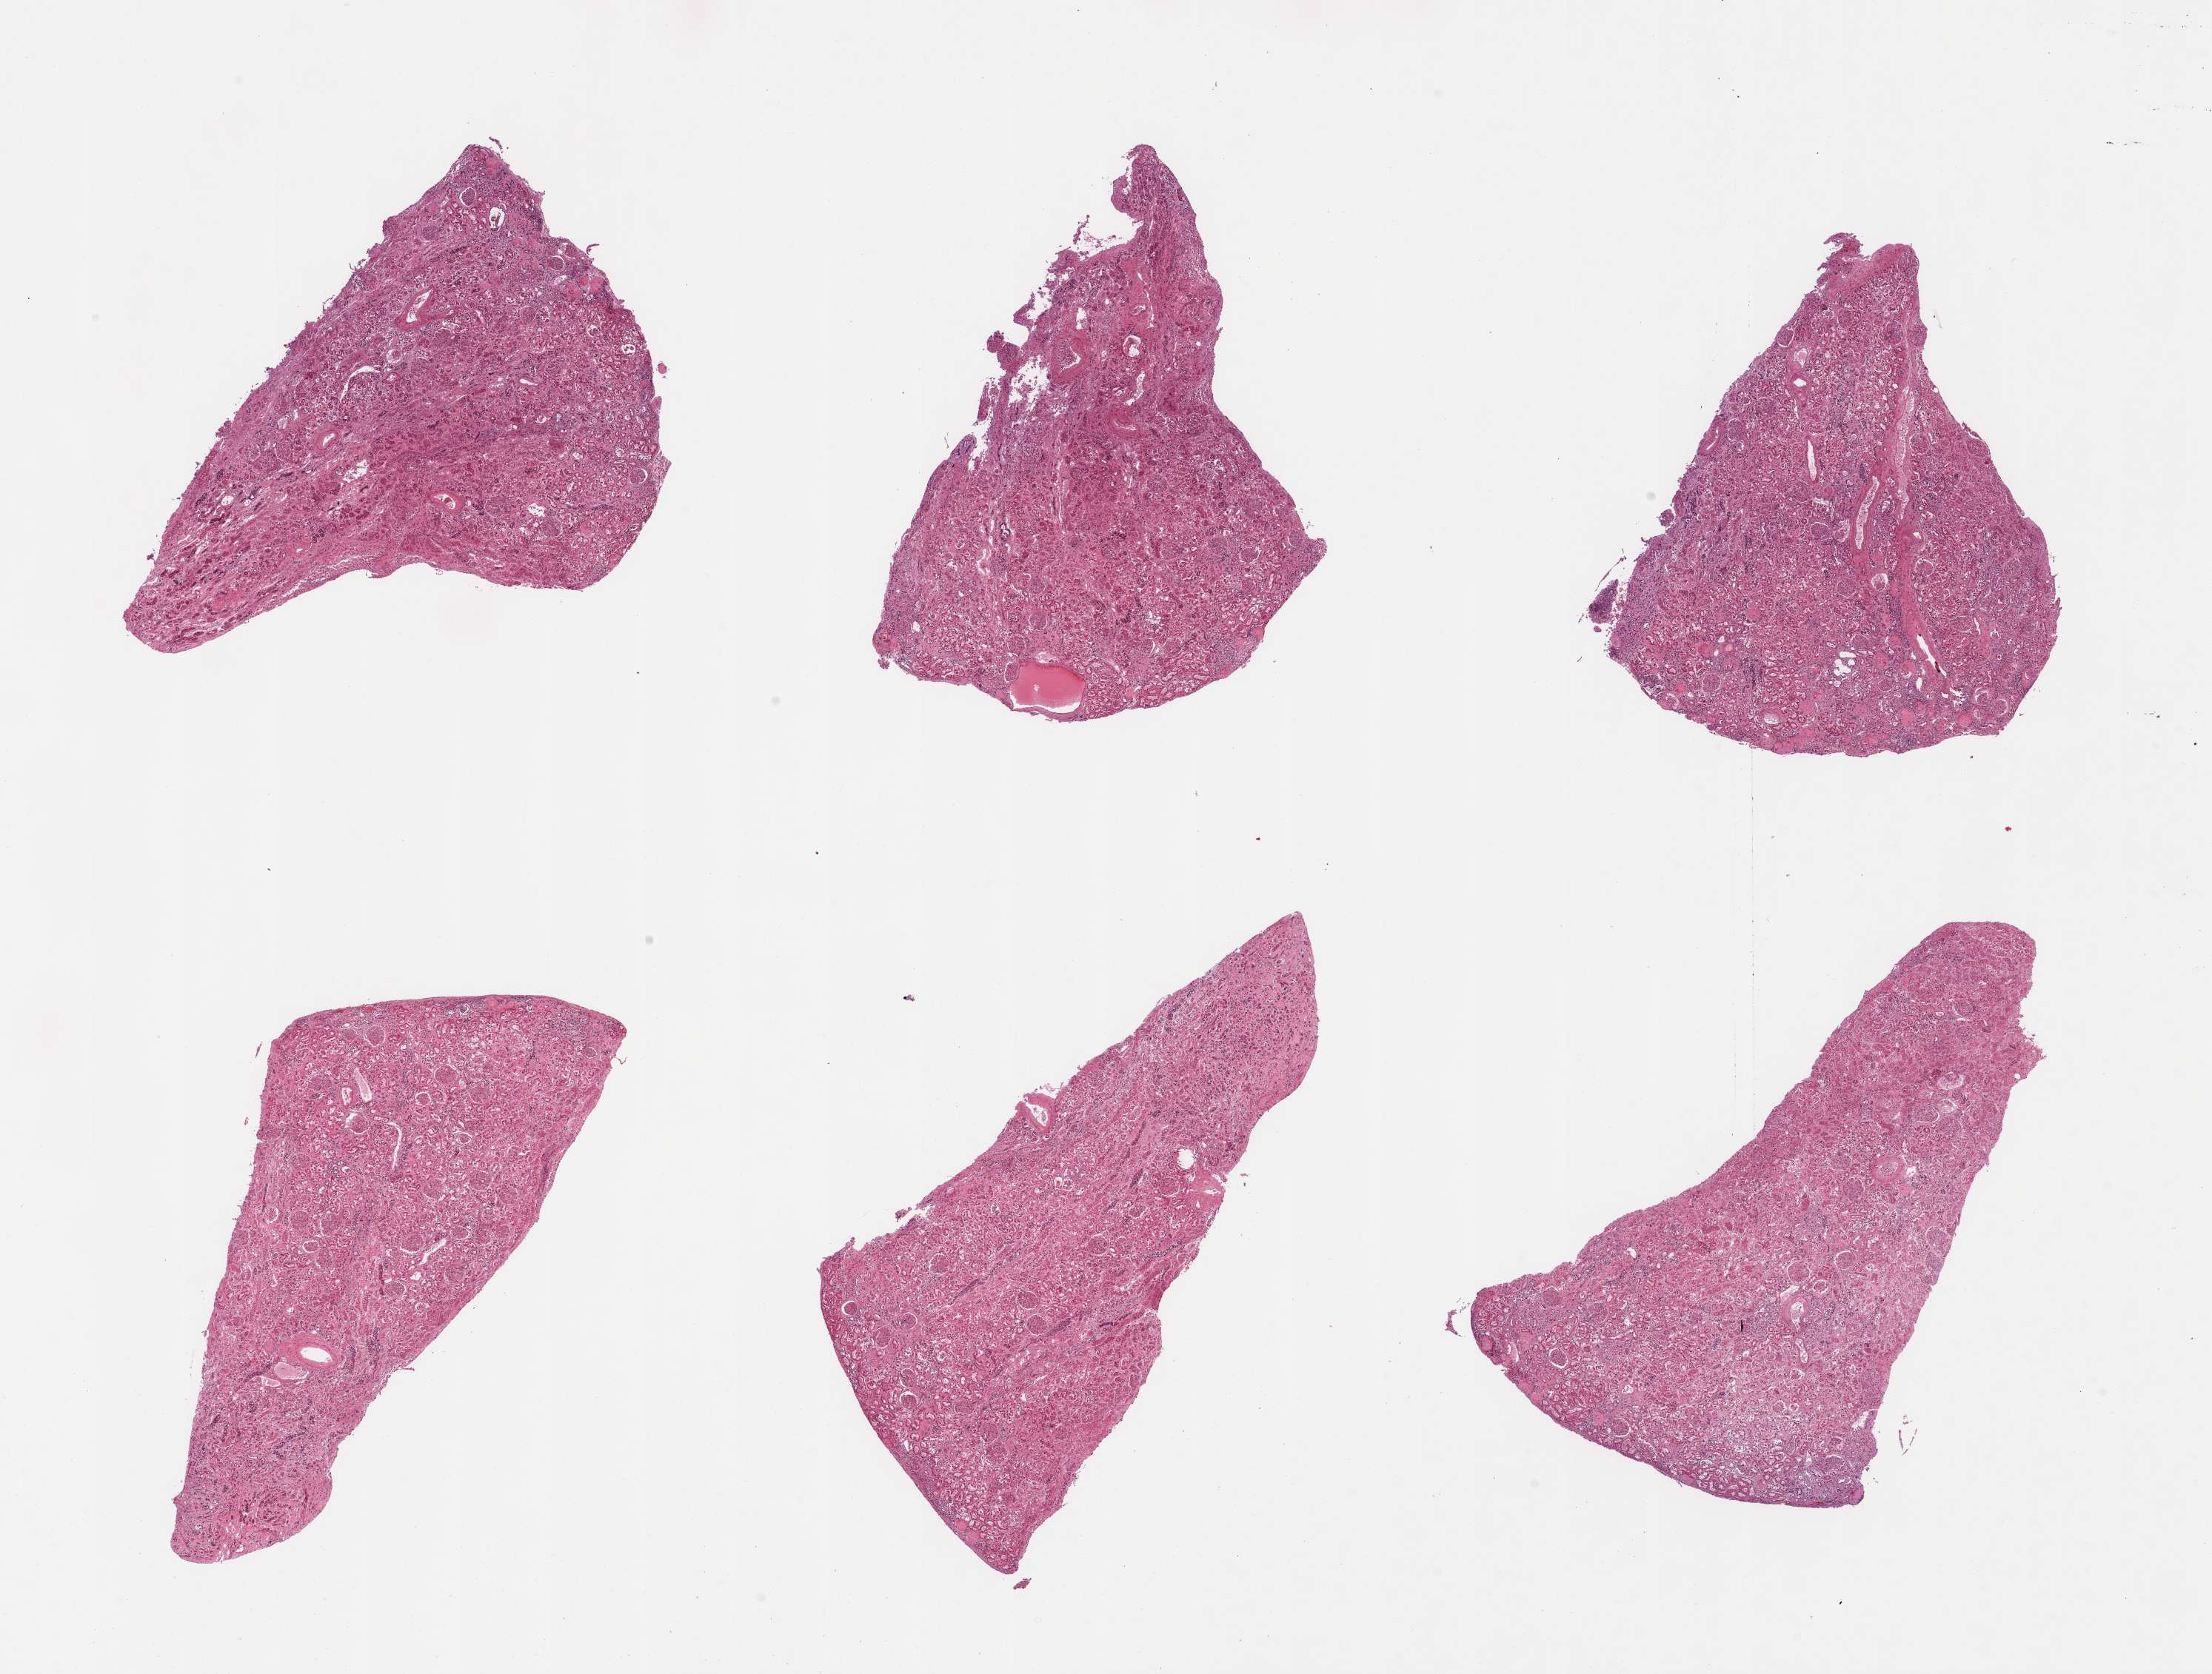
Whole-slide image, hematoxylin and eosin (H&E) stain, brightfield — low-resolution overview of the scanned area, about 23.6 x 17.9 mm (from a 20x scan), PAXgene-fixed, paraffin-embedded tissue, sampled site (target tissue): renal cortex, tissue donor sample. Donor sex: female.
Reviewer comment on this tissue sample: 6 pieces; KIDNEY not spleen; tubules severely autolyzed, glomeruli largely intact.